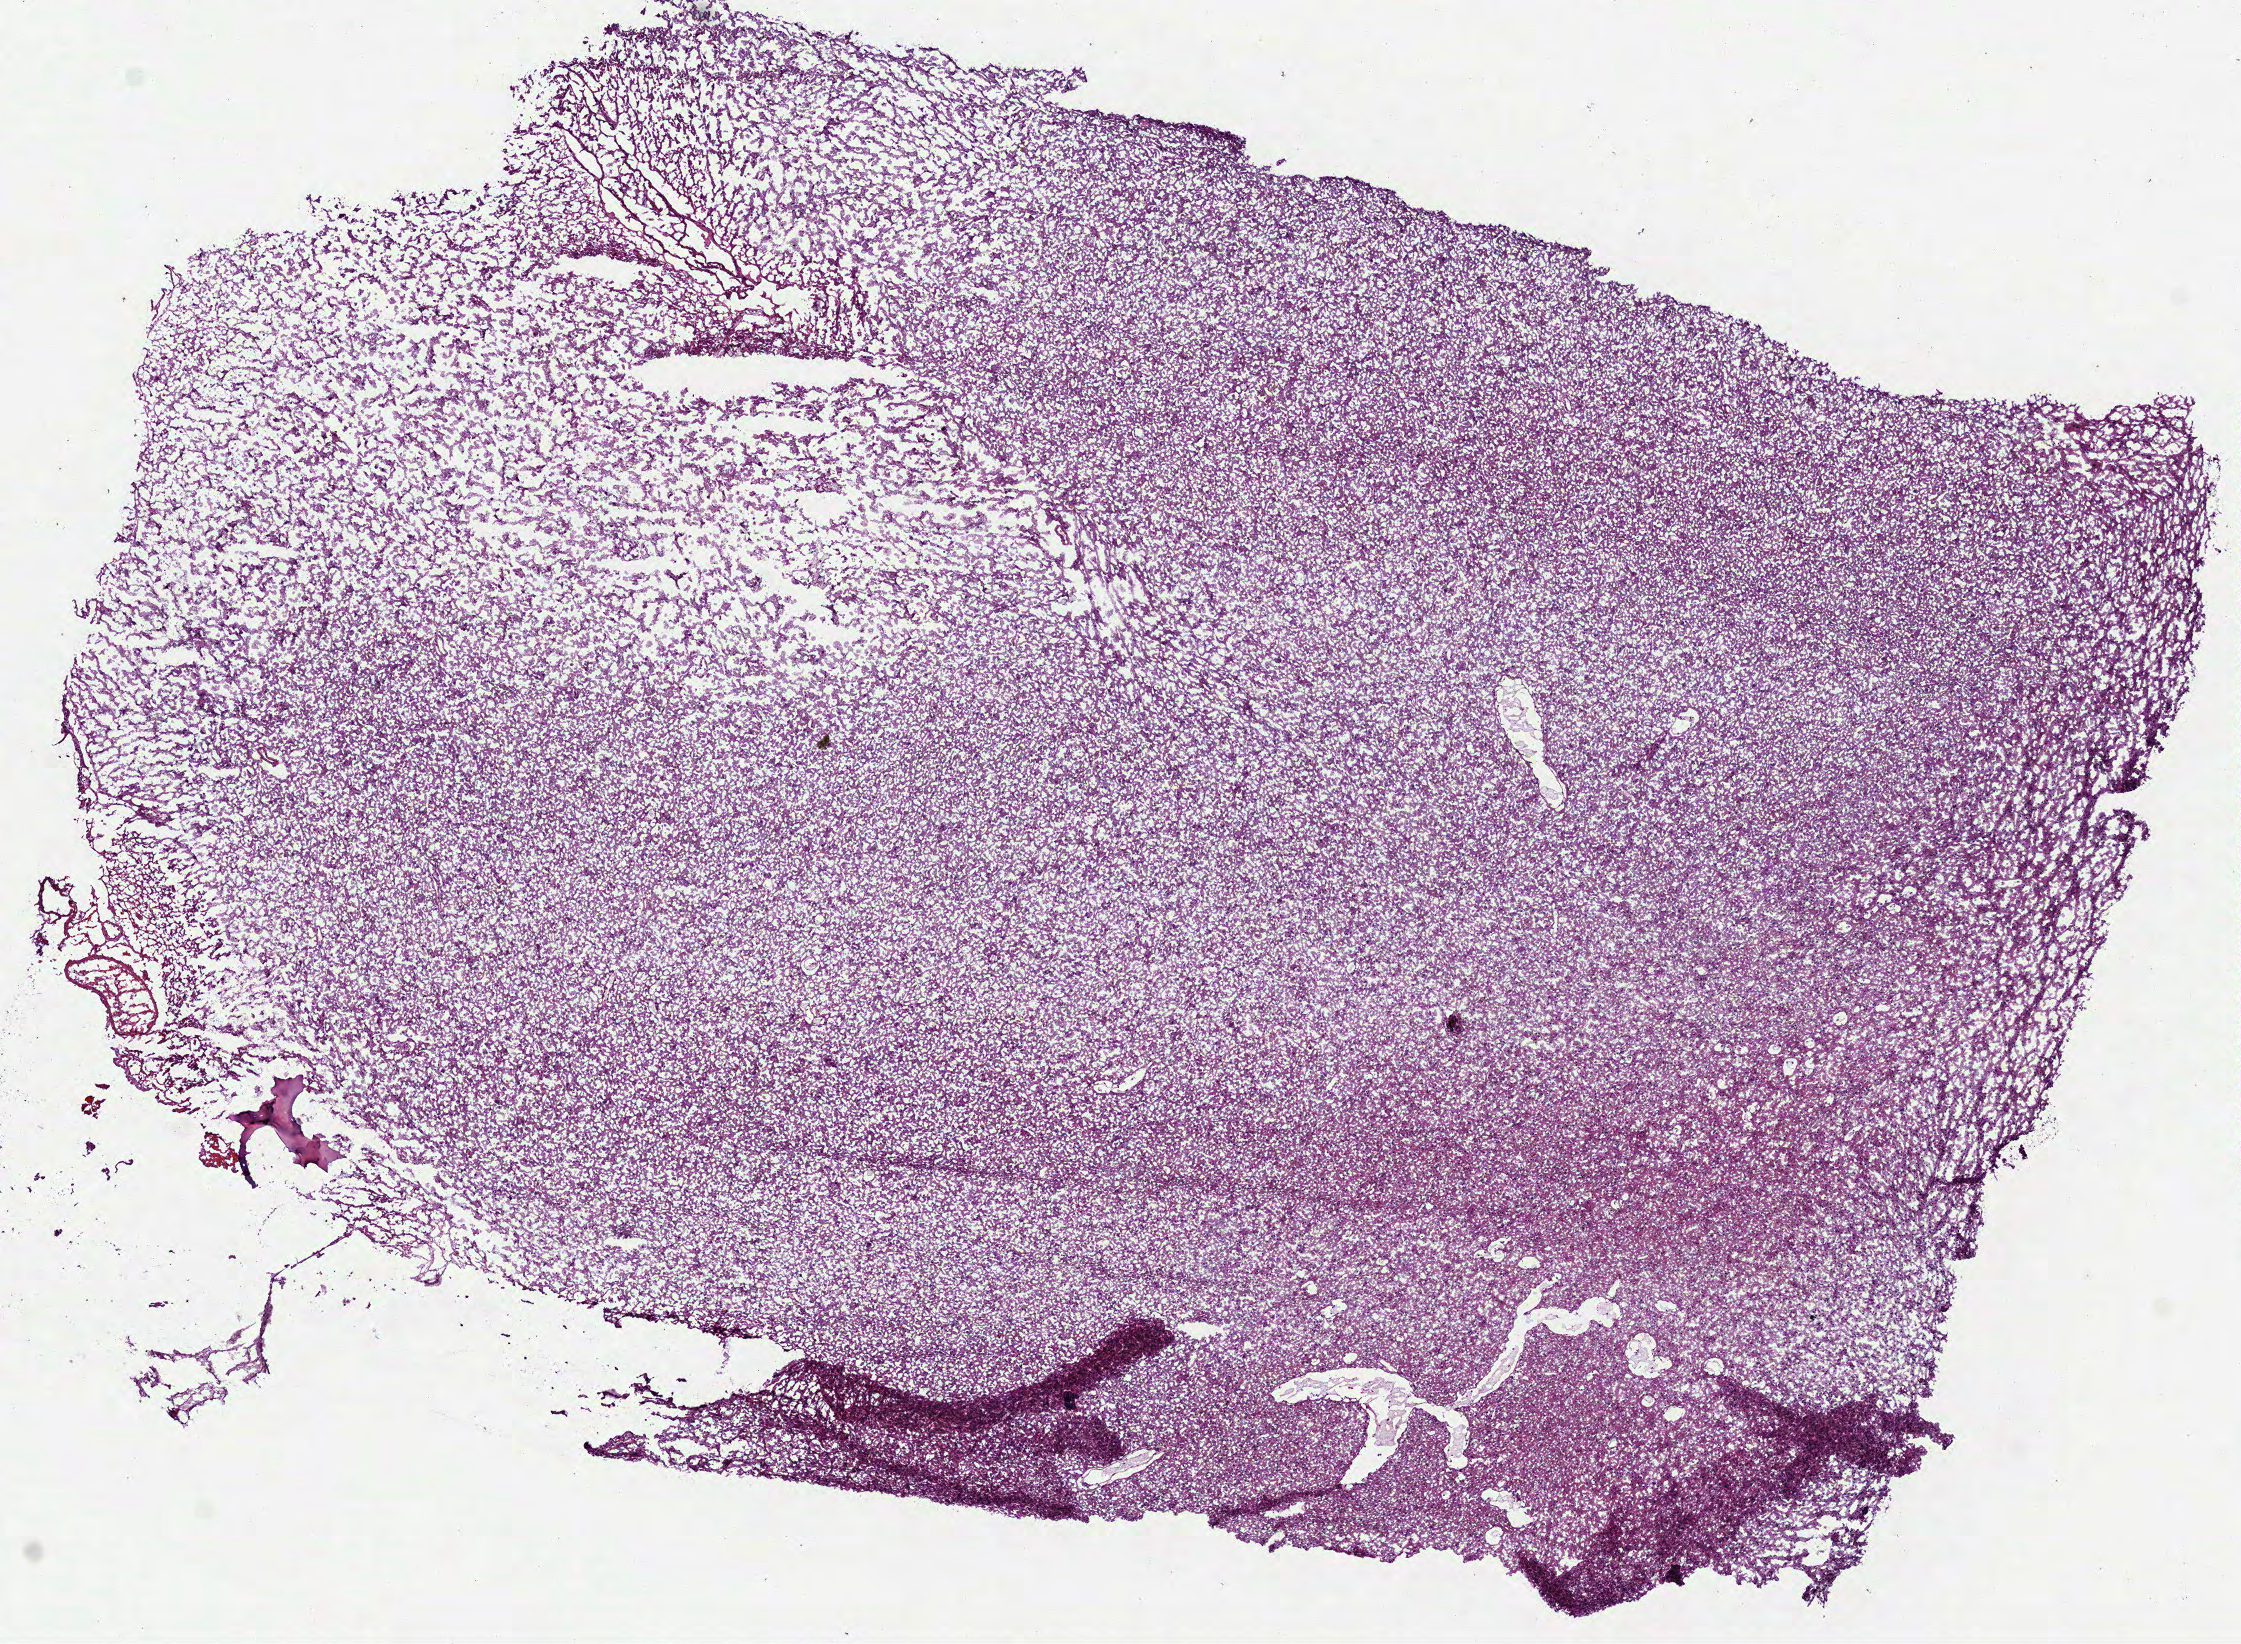
H&E whole-slide image, a low-resolution overview of the entire scanned area, about 9.0 x 6.6 mm. Frozen section from the bottom of the tissue portion. Sample: primary tumour, brain. Female patient; age at initial diagnosis 44 years. Slide review estimates, as recorded: tumour cells 100%, tumour nuclei 60%, normal cells 0%, stromal cells 0%, necrosis 0%.
• diagnosis: Glioblastoma